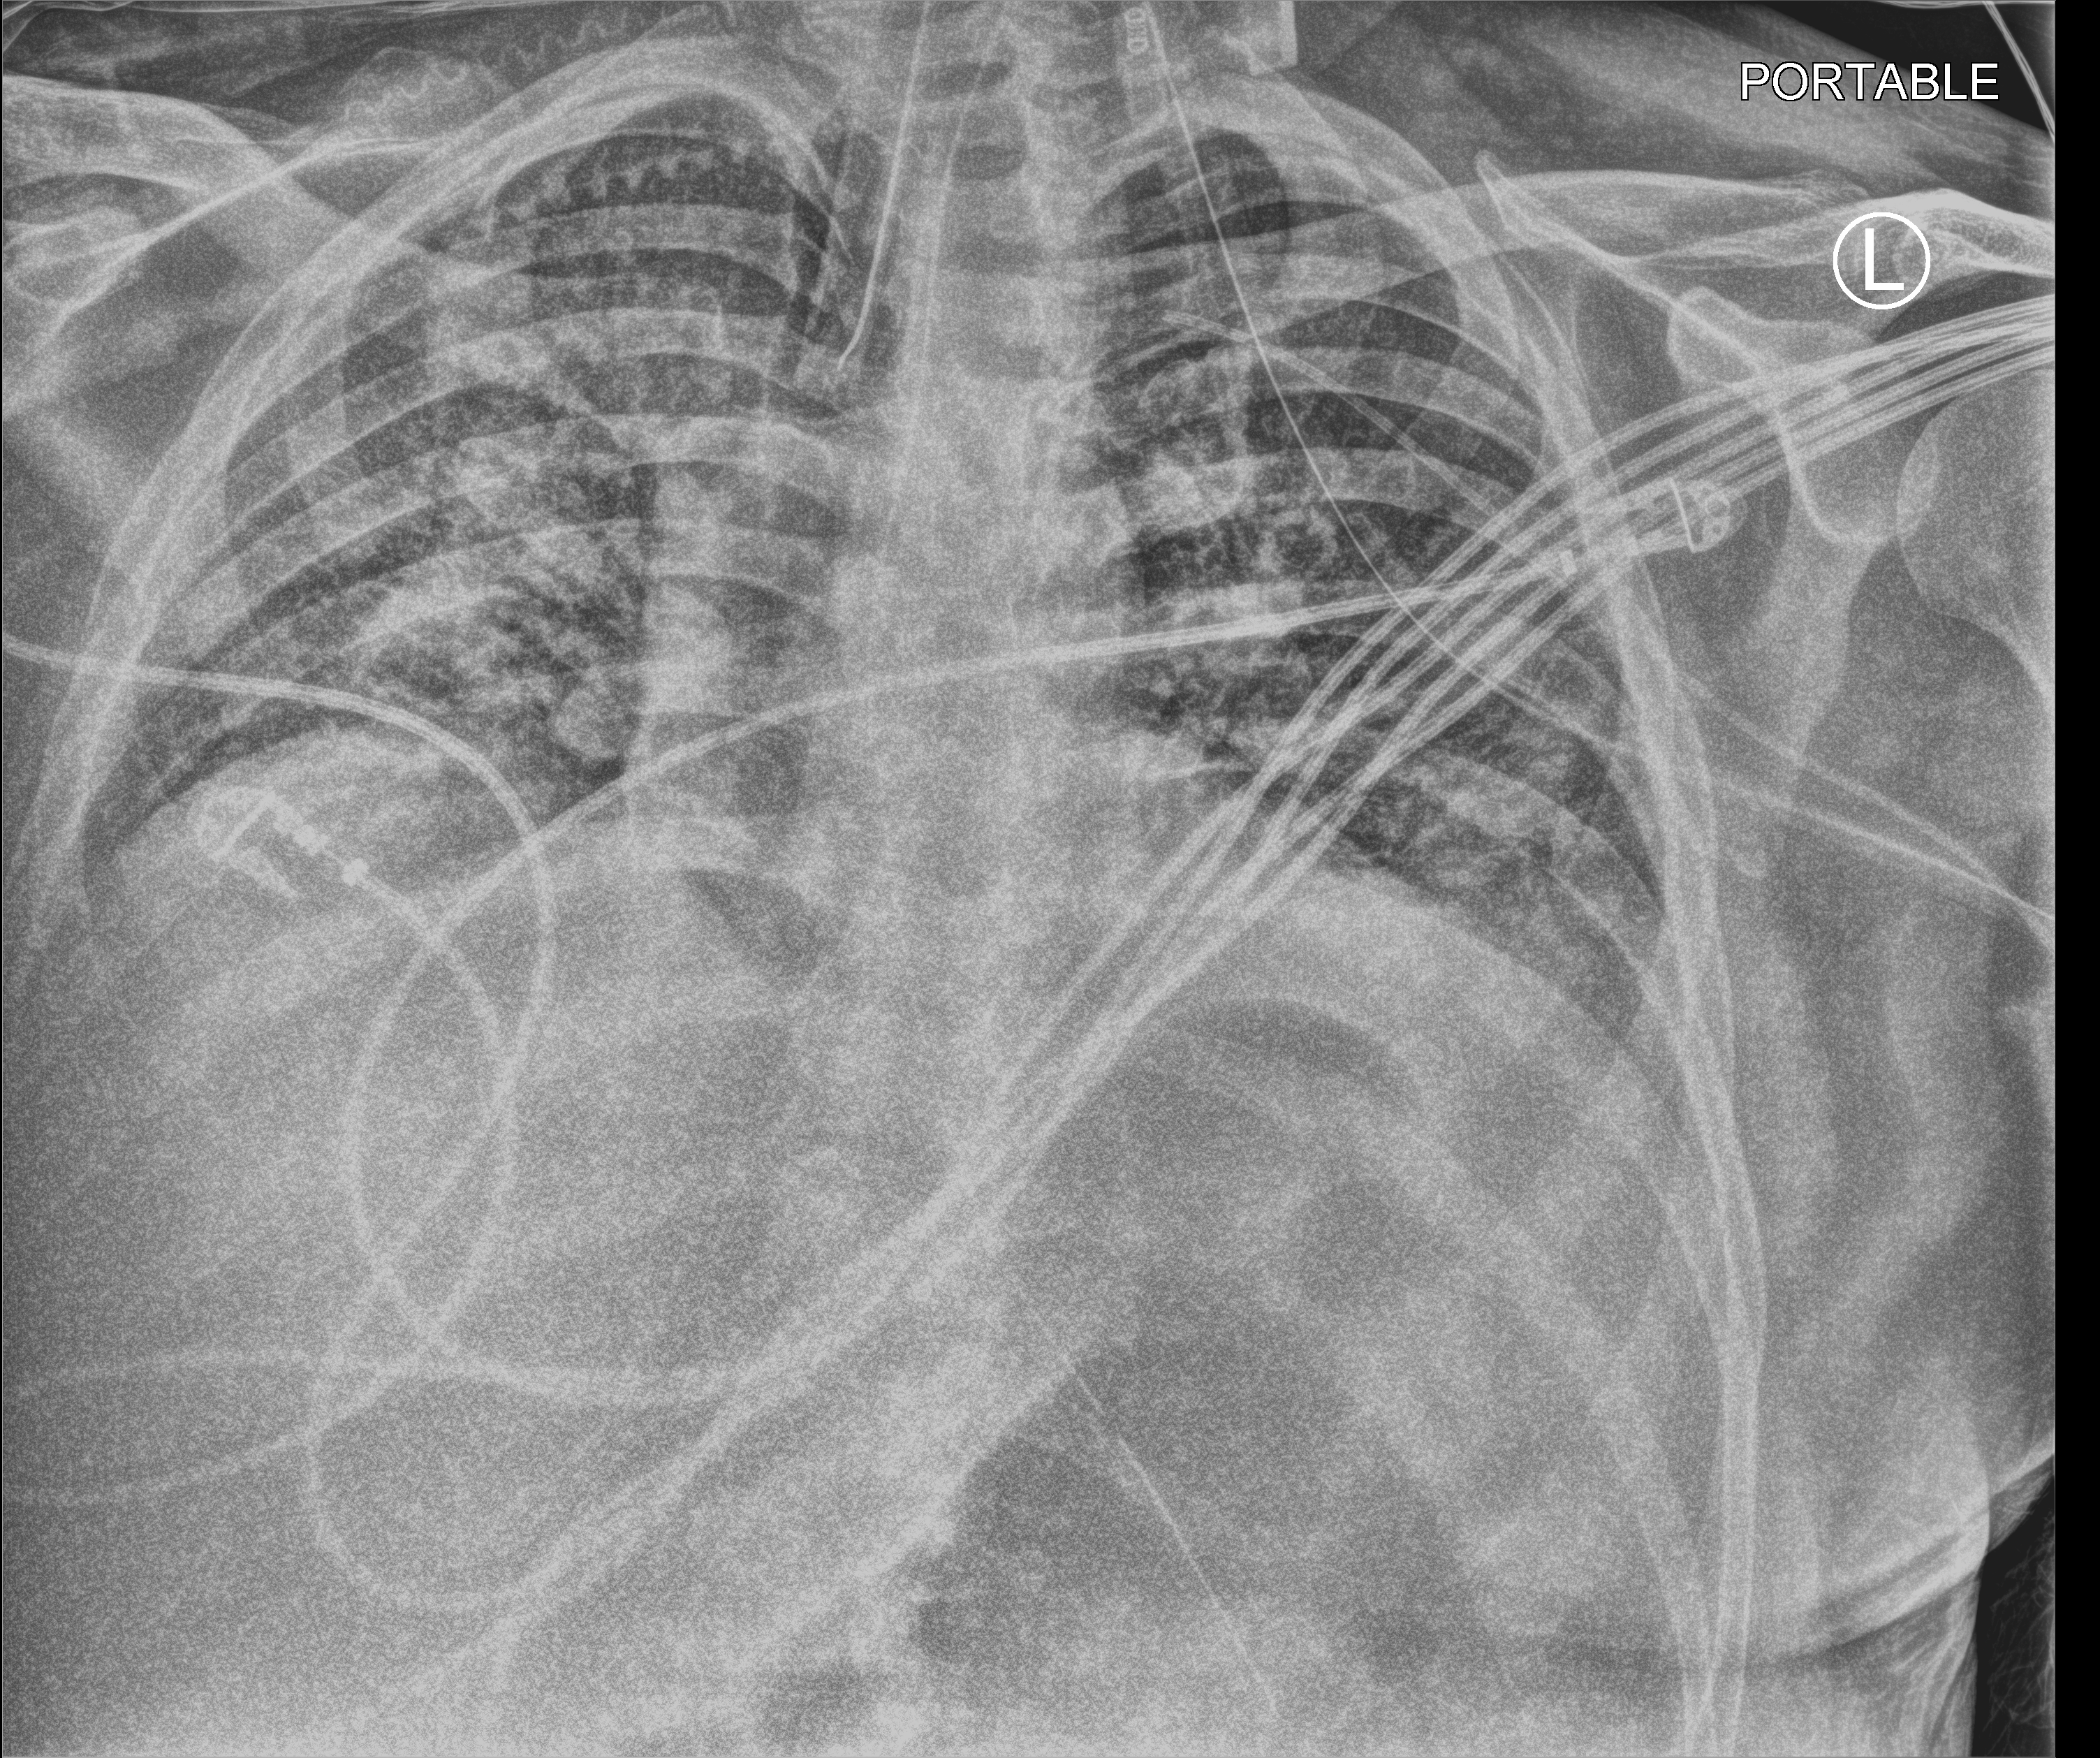
Bedside chest radiograph (computed radiography); anteroposterior (AP) projection. Male patient hospitalised with COVID-19, age 18–59 years.
From the hospital-stay record, not from the radiograph (when in the stay this image was taken is not recorded): length of hospital stay: 80 days; other chronic lung disease (admission record): no; smoking status (admission record): never.